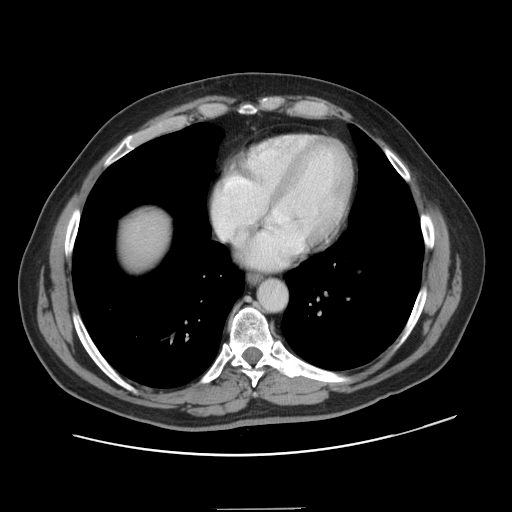
Contrast-enhanced abdominal CT, one axial slice; slice 142 of 143 in the series (ordered by position); 120 kVp; intravenous contrast given; soft-tissue window (W 400 / L 40 HU); 2.5 mm slice thickness; 512 × 512 image matrix, field of view 402 × 402 mm. Male patient, age 62 years. From the clinical record (not read from this slice): diagnosis: colorectal cancer liver metastases, imaged before liver resection; multiple liver metastases: yes.
Outlined on this slice (manually delineated by an expert):
- liver: box from (x=120, y=214) to (x=168, y=271) px
- planned liver remnant (the part of the liver to remain after resection): (x=120, y=214)–(x=167, y=272)